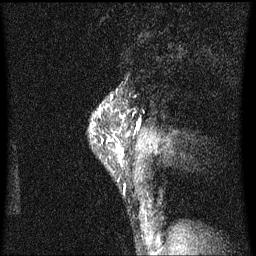
Breast MRI (dynamic contrast-enhanced), one sagittal slice. Position 51 of 60 along the scan axis. Dynamic contrast-enhanced series, image 2 of 3 at this slice position (ordered by acquisition). 1.5 T. TE 4.2 ms, TR 8.4 ms. 2 mm slice thickness. 256 × 256 image matrix. Female patient, age 40 years.
Outlined on this slice (semi-automatic segmentation, software-assisted and operator-edited):
- analysis volume of interest (the breast-tissue region the enhancement analysis was run in; not a lesion): bounding box [x1, y1, x2, y2] px = [92, 94, 125, 163]
- tumour enhancement mask (voxels above the 70 % enhancement threshold inside the analysis volume of interest): [100, 112, 125, 163]